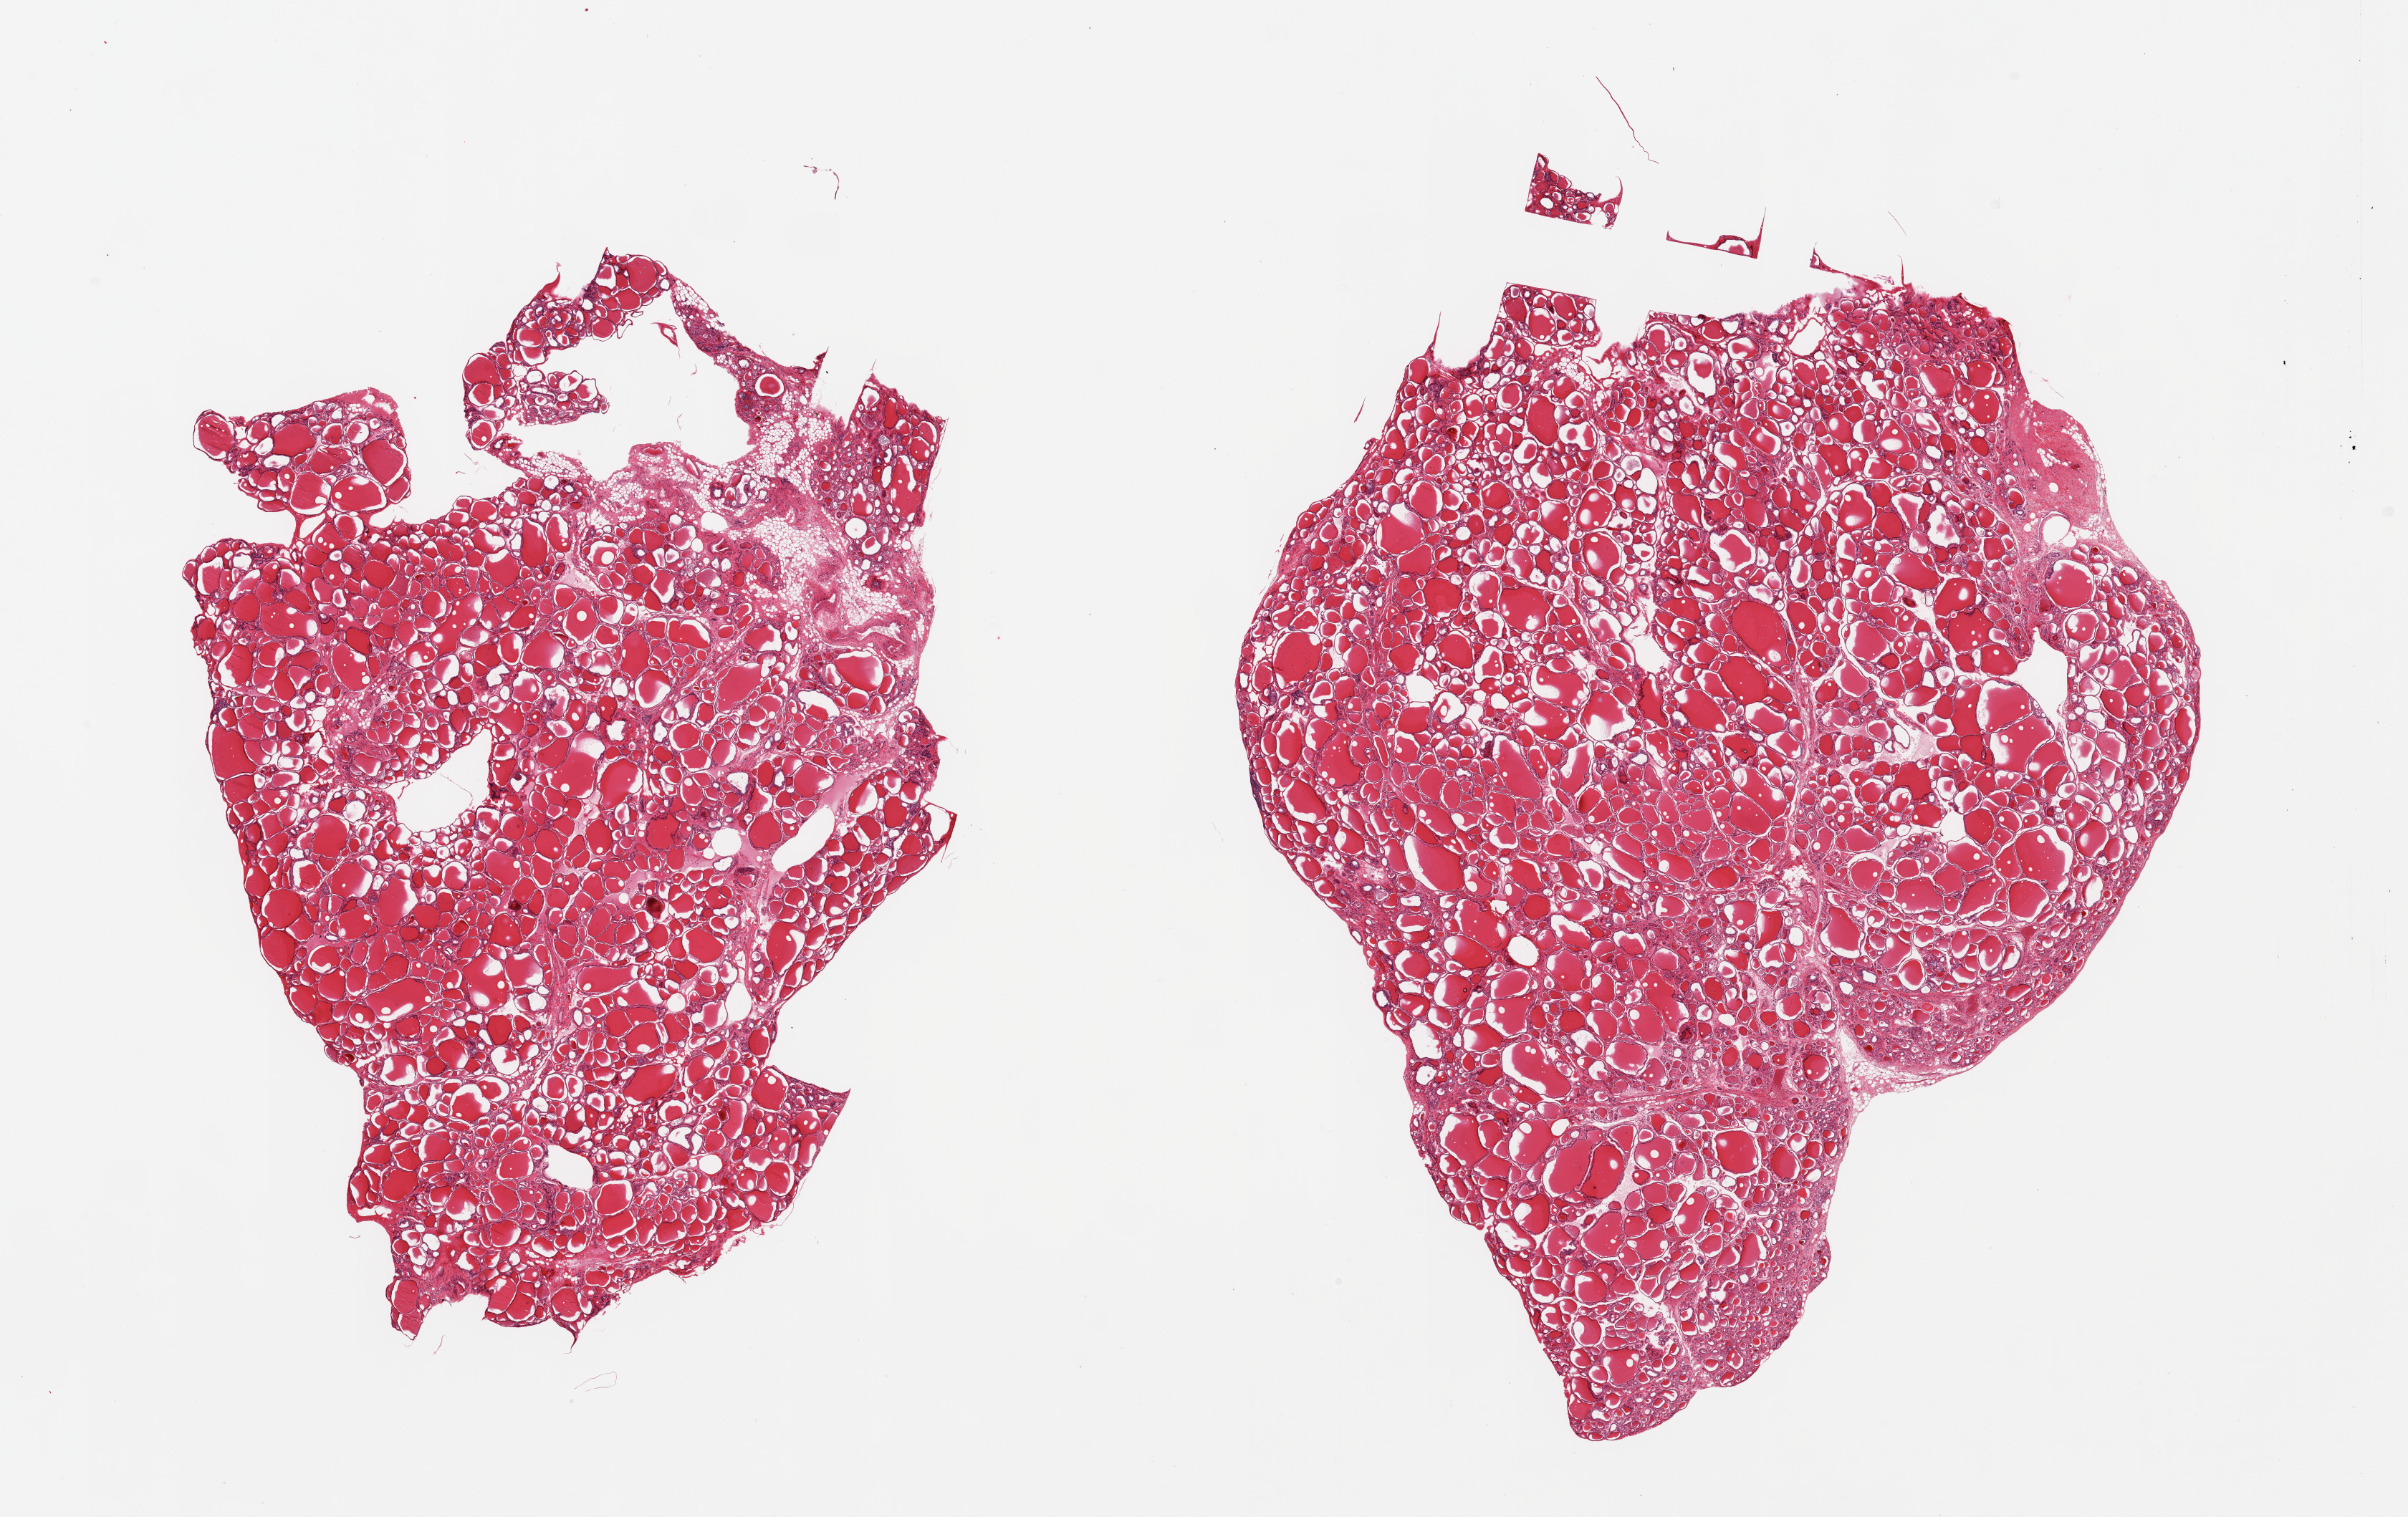
Whole-slide image, haematoxylin and eosin stain — a low-resolution overview of the entire scanned area, about 26.6 x 16.7 mm; PAXgene-fixed, paraffin-embedded tissue; section of thyroid (target tissue); donor tissue sample. Donor: male.
Review note (as recorded): 2 pieces; 5-10% of one piece is fat/vessels.